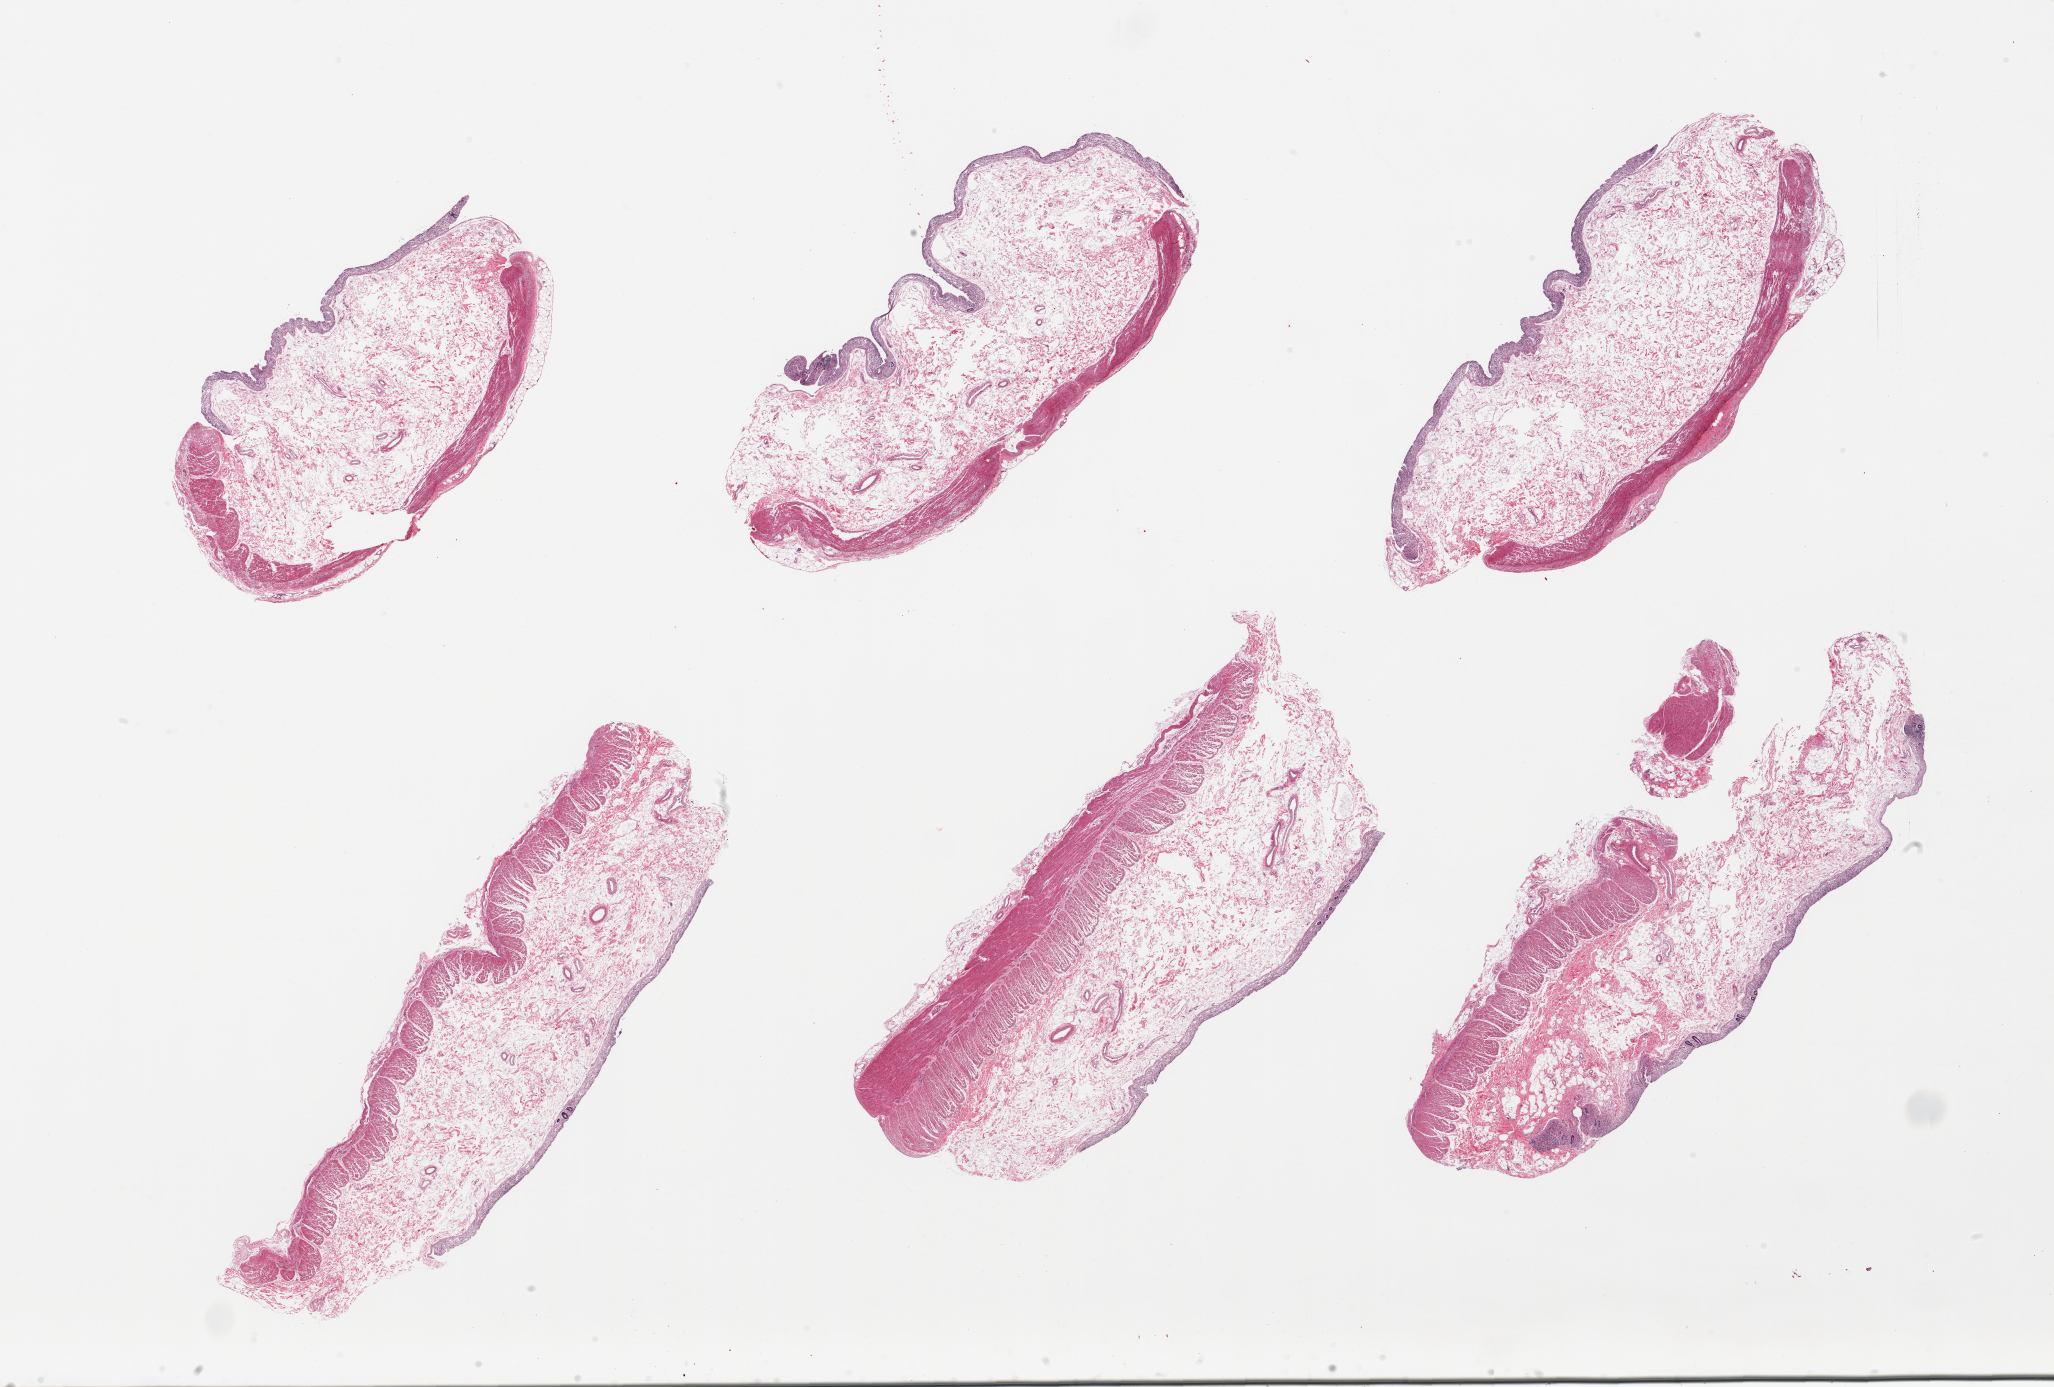
H&E whole-slide image, shown as a low-resolution overview of the whole scanned area (about 32.5 x 21.9 mm, from a 20x scan), PAXgene-fixed, paraffin-embedded tissue, target tissue: transverse colon, tissue donor sample. Donor: male.
Review note (as recorded): 6 pieces; edema, mucosal autolysis.